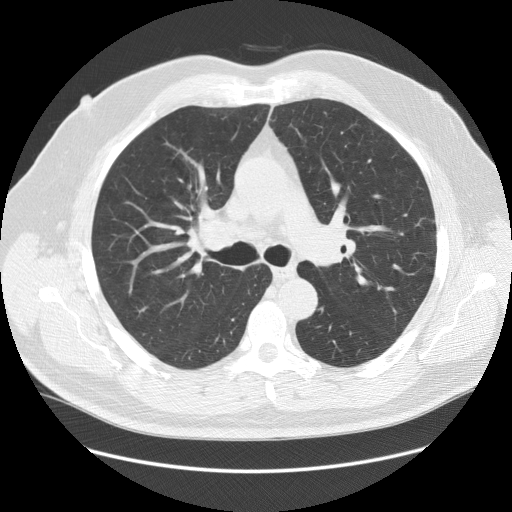
Axial slice from a low-dose chest CT screening exam. First (baseline) screen. Lung window (W 1500 / L -600 HU). Standard (soft-tissue) reconstruction kernel (STANDARD). Slice 51 of 140 in the series. Male, age 64 years at enrolment.
• Lesion marked by an expert reader, bounding box <179,203,250,271> (left, top, right, bottom; pixels).
• The exam's reader record, not a measurement of the box and not confirmed to be the same lesion: non-calcified nodule or mass ≥4 mm, right lower lobe, 7 × 5 mm, smooth margins, soft tissue attenuation.
• Official screen result: positive, change unspecified: nodule(s) >= 4 mm or enlarging nodule(s), mass(es), or other non-specific abnormalities suspicious for lung cancer.
• Later outcome: lung cancer diagnosed 456 days after this screen (after the second annual screen) — adenocarcinoma, NOS, right upper lobe, poorly differentiated (G3), stage IB (AJCC 6th edition), 37 mm at pathology.